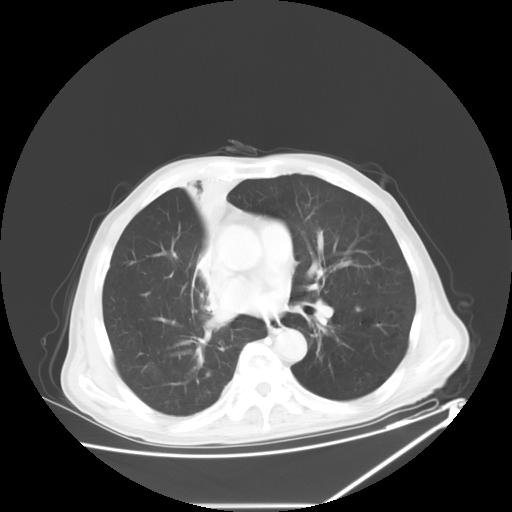
Chest CT, one axial slice. Position 33 of 60 along the scan axis. Reconstruction kernel STANDARD. Lung window (W 1500 / L -600 HU). 5 mm slice thickness. 512 × 512 image matrix, field of view 410 × 410 mm. Male patient, age 73 years. From the clinical record (not read from this slice): clinical TNM (as recorded): T2a N1 M0.
Annotated regions visible in this slice (rectangle marked by the reading radiologist):
- lung tumour (recorded histology: squamous cell carcinoma): bounding box (x1, y1, x2, y2) in pixels: (167, 162, 241, 339)